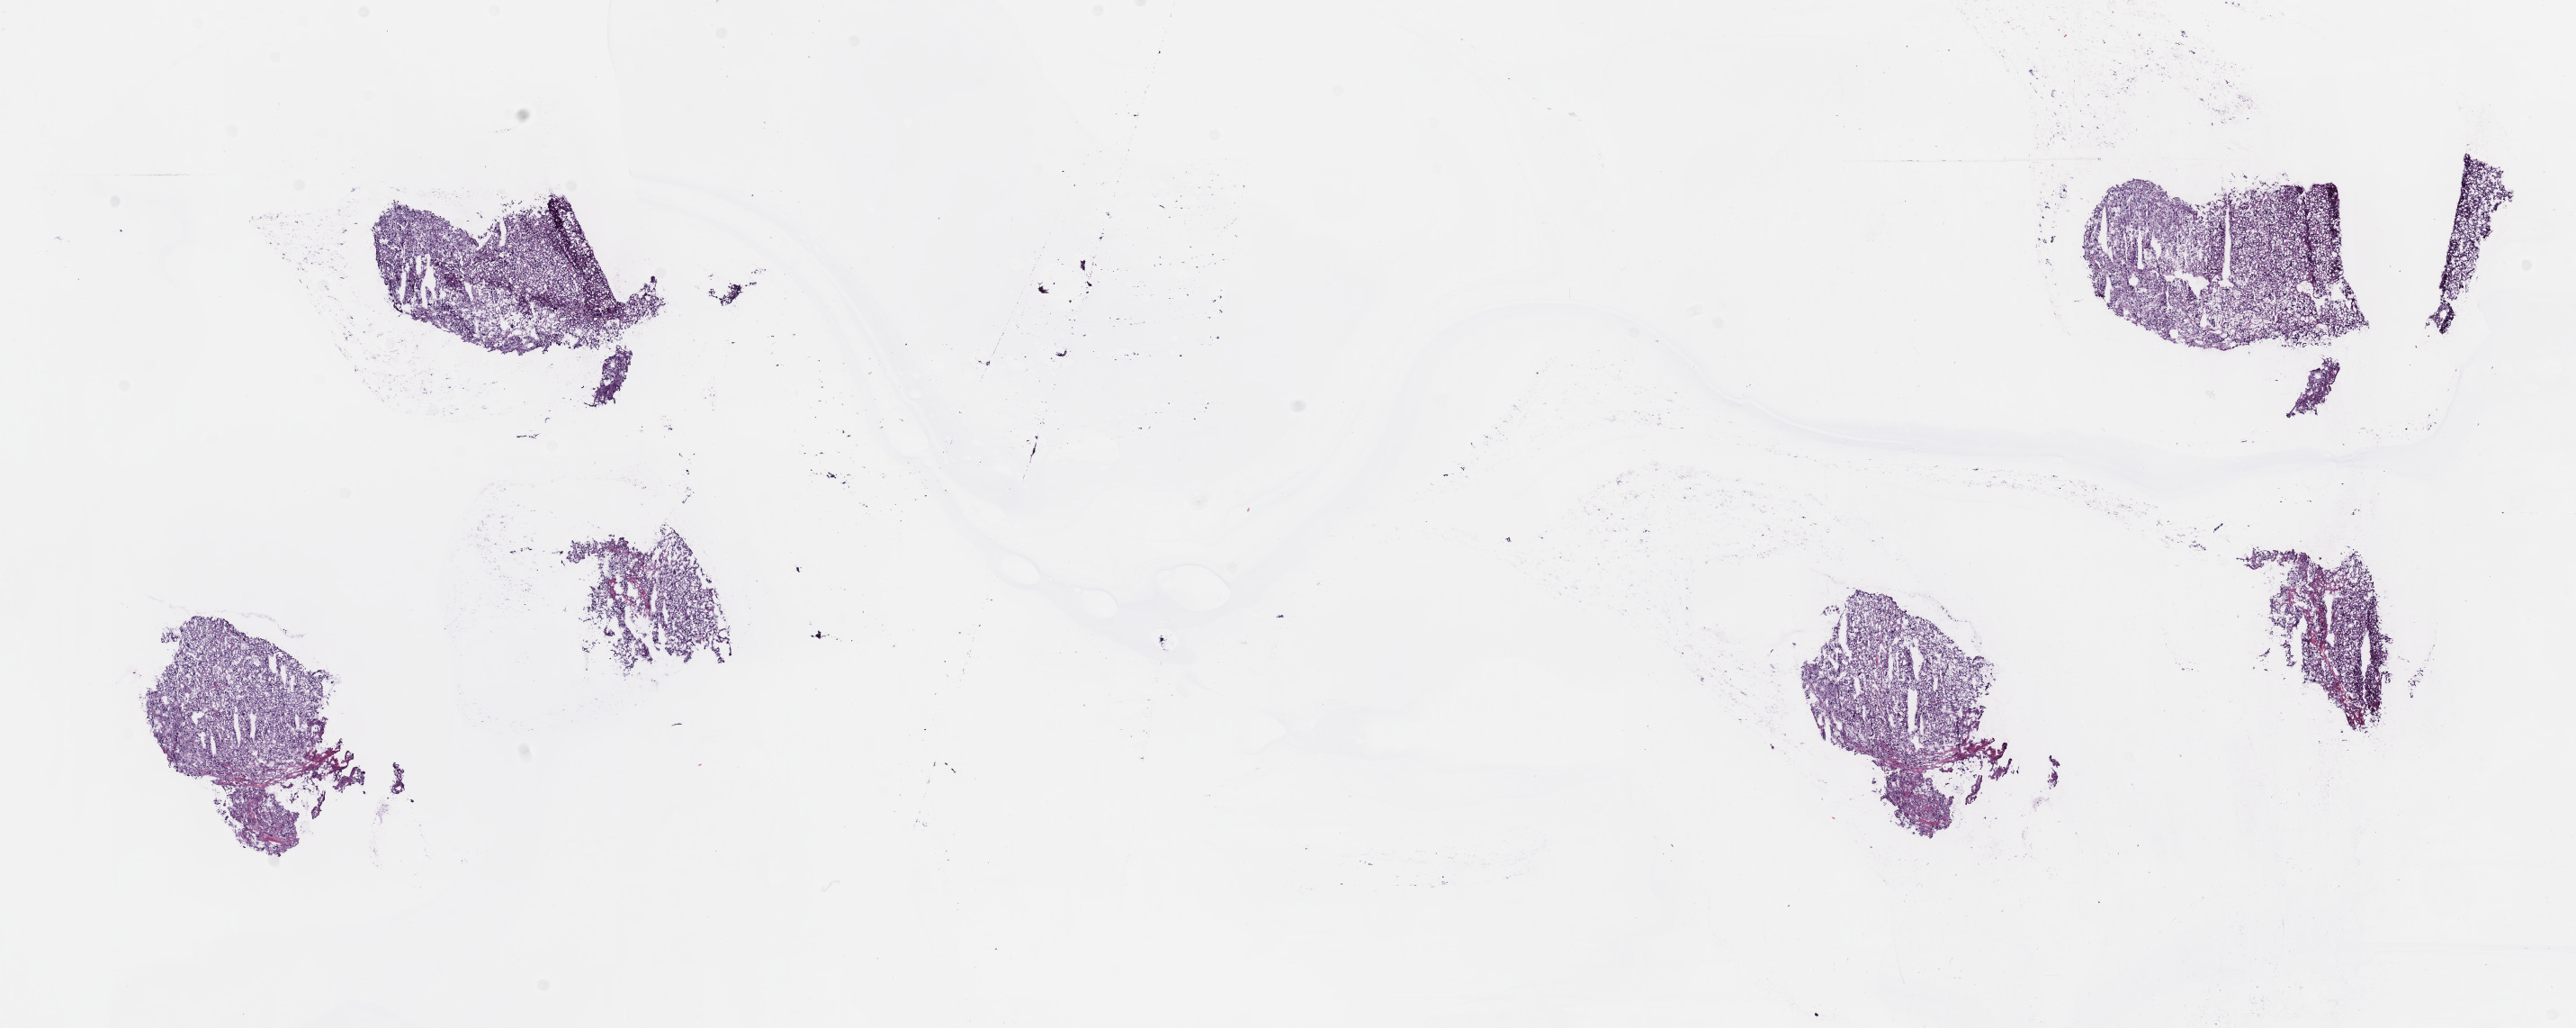
Whole-slide histology image, H&E, whole scanned area (about 23.2 x 9.2 mm, acquisition: 40x scan) shown as a low-resolution overview; frozen section from the top of the tissue portion; primary tumour sample from the adrenal gland. Female, age 28 years at initial diagnosis. Composition of this section per pathologist review: tumour cells 100%, tumour nuclei 80%.
Pathologic diagnosis: Pheochromocytoma, NOS.